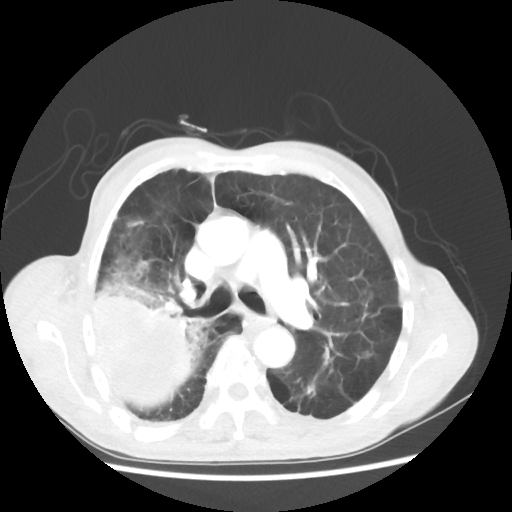
Chest CT, one axial slice; position 34 of 58 along the scan axis; 100 kVp; lung window (W 1500 / L -600 HU); 512 × 512 image matrix, field of view 351 × 351 mm. Patient: male, 75 years. Case-level facts recorded for this patient, not image findings: clinical TNM (as recorded): T4 N1 M1.
Outlined on this slice (rectangle marked by the reading radiologist):
- lung tumour (recorded histology: adenocarcinoma): bounding box (x1, y1, x2, y2) in pixels: (88, 267, 216, 414)